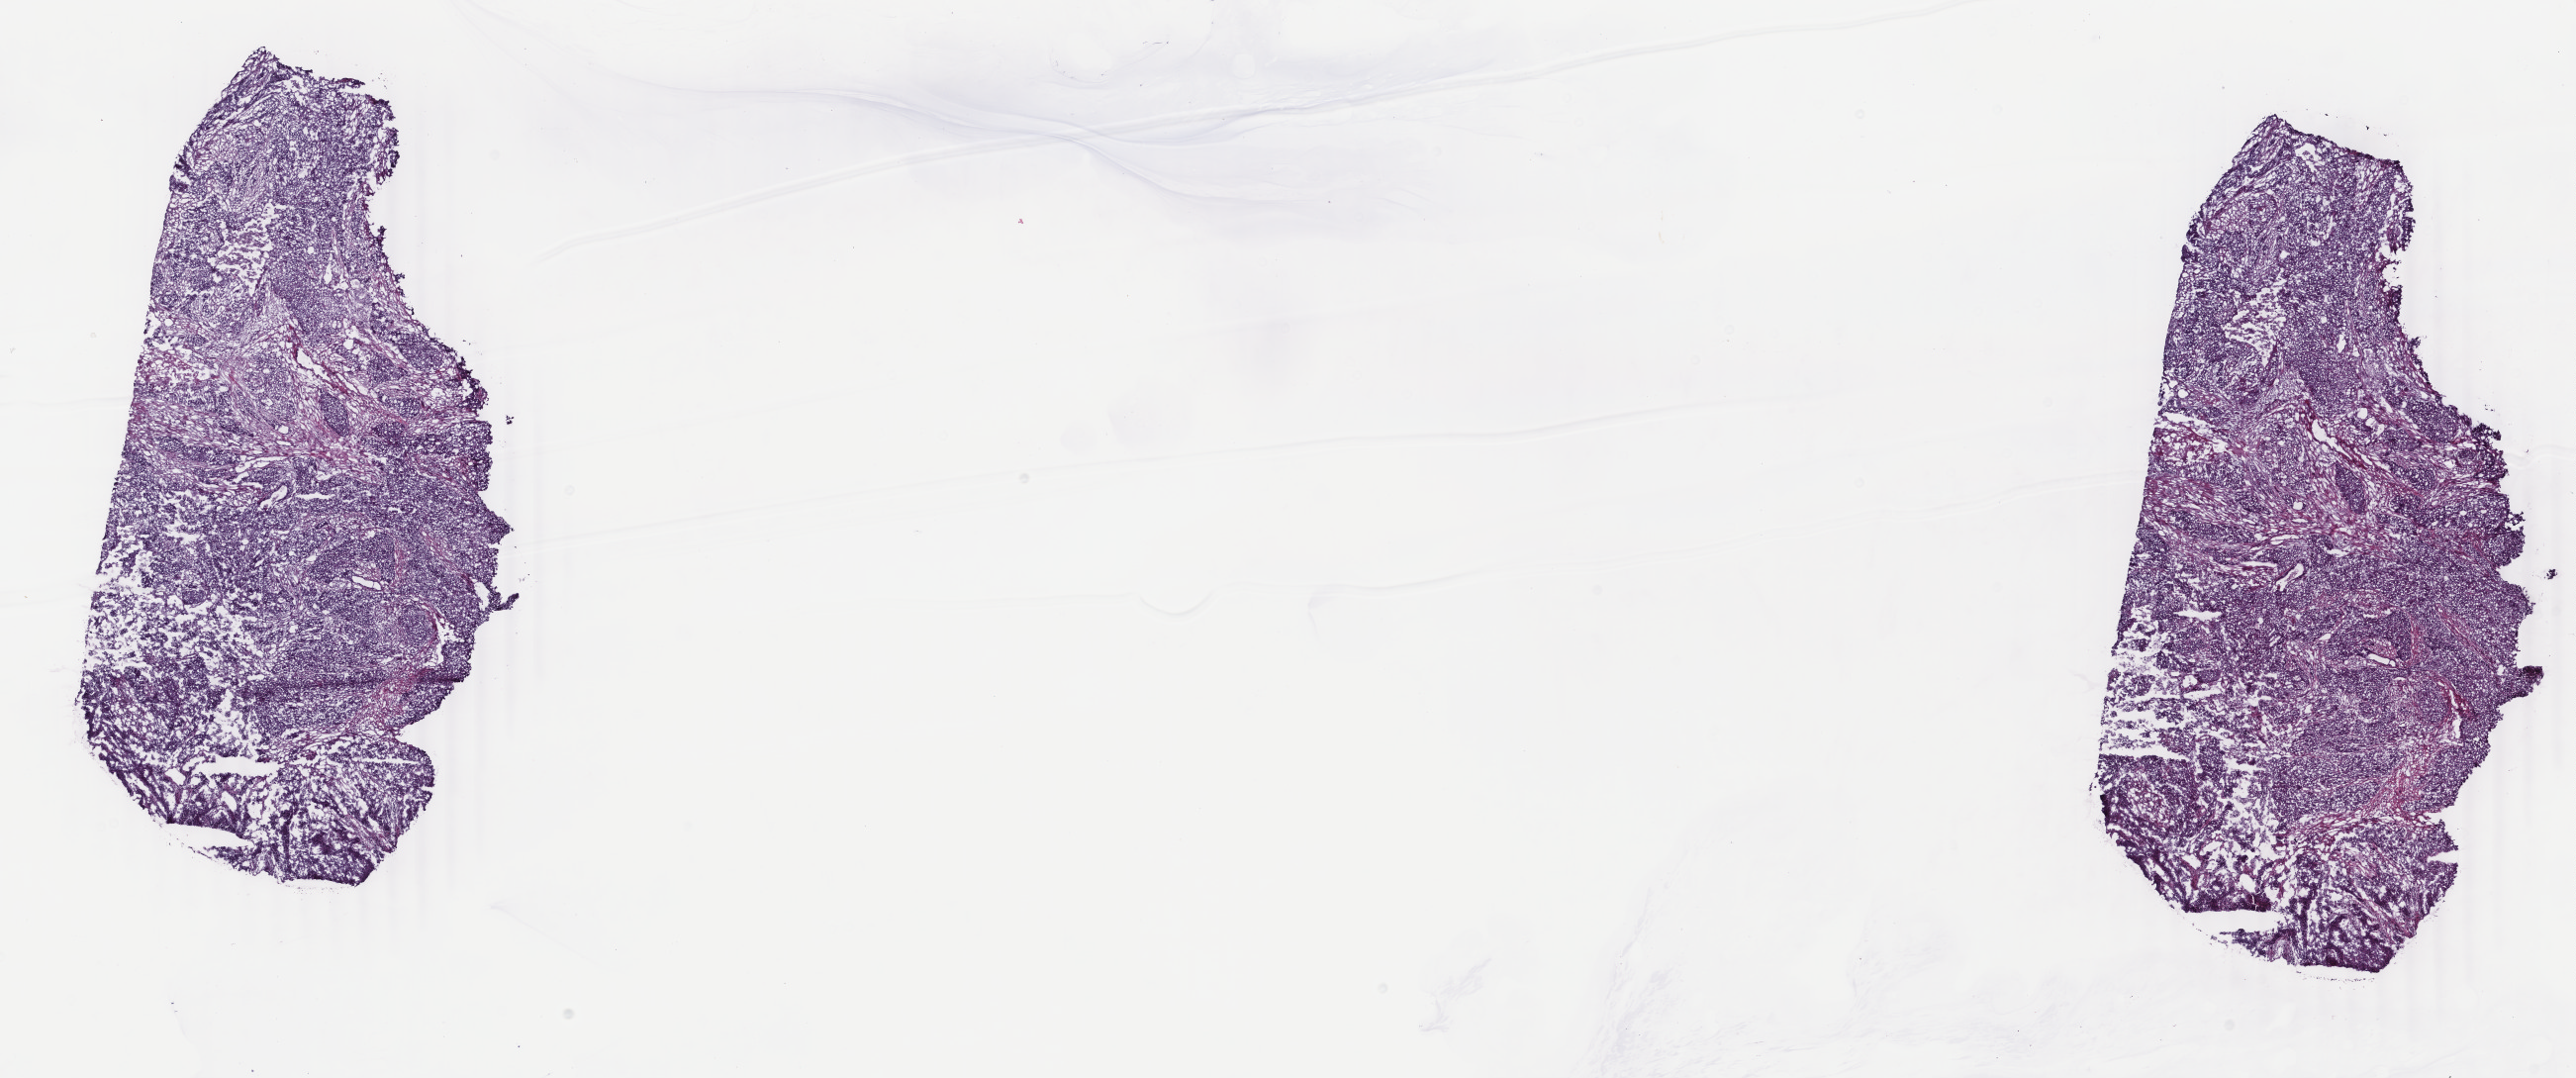
Digitized Hematoxylin and eosin (H&E) stained tissue section (whole slide), low-resolution overview of the scanned area, about 20.7 x 8.7 mm, frozen section from the top of the tissue portion, uterus, primary tumour sample. Female, age 67 years at initial diagnosis. Histologic grade: G3 (poorly differentiated). Pathologist review of this section (percent, as recorded): tumour cells 72%, tumour nuclei 80%, normal cells 5%, stromal cells 20%, necrosis 3%. Infiltration values recorded for this section: lymphocyte infiltration 8%, monocyte infiltration 1%, neutrophil infiltration 2%.
- histologic diagnosis: Endometrioid adenocarcinoma, NOS (endometrium)
- FIGO stage: IB
- lymph nodes positive (case pathology): 0 of 10 examined